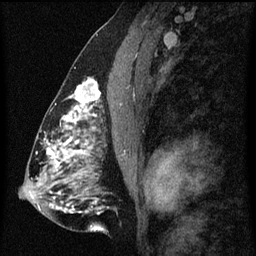
Breast MRI (dynamic contrast-enhanced), one sagittal slice. Position 32 of 60 along the scan axis. Dynamic contrast-enhanced series, image 2 of 3 at this slice position (ordered by acquisition). 1.5 T. TE 4.2 ms, TR 8 ms. 2 mm slice thickness. 256 × 256 image matrix. Patient: female, 51 years.
Structures marked on this image (semi-automatically segmented with operator editing):
- analysis volume of interest (the breast-tissue region the enhancement analysis was run in; not a lesion): box from (x=61, y=78) to (x=102, y=129) px
- tumour enhancement mask (voxels above the 70 % enhancement threshold inside the analysis volume of interest): (x=61, y=78)–(x=101, y=125)